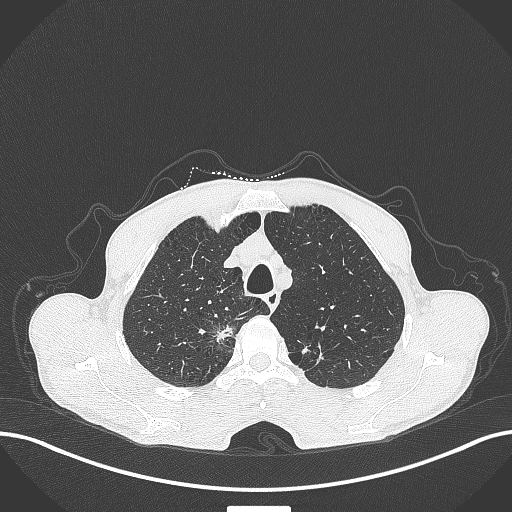
Chest CT, one axial slice. Slice 349 of 445 in the series (ordered by position). Reconstruction kernel B70f. 120 kVp. Lung window (W 1500 / L -600 HU). 1 mm slice thickness. 512 × 512 image matrix, field of view 400 × 400 mm. Patient: male, 70 years. From the clinical record (not read from this slice): clinical TNM (as recorded): T1a N0 M0.
Outlined on this slice (rectangle marked by the reading radiologist):
- lung tumour (recorded histology: adenocarcinoma): box from (x=212, y=319) to (x=237, y=345) px